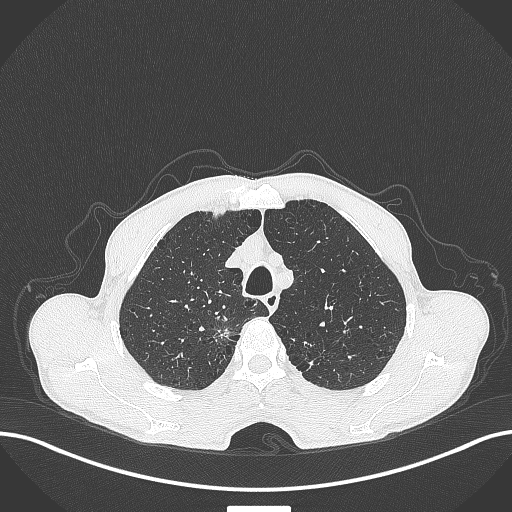
Chest CT, one axial slice; slice 343 of 445 in the series (ordered by position); 120 kVp; lung window (W 1500 / L -600 HU); 512 × 512 image matrix. Male patient, age 70 years. Case-level facts recorded for this patient, not image findings: clinical TNM (as recorded): T1a N0 M0; histopathological grade: G1-2.
Outlined on this slice (rectangle marked by the reading radiologist):
- lung tumour (recorded histology: adenocarcinoma): box from (x=214, y=321) to (x=238, y=348) px